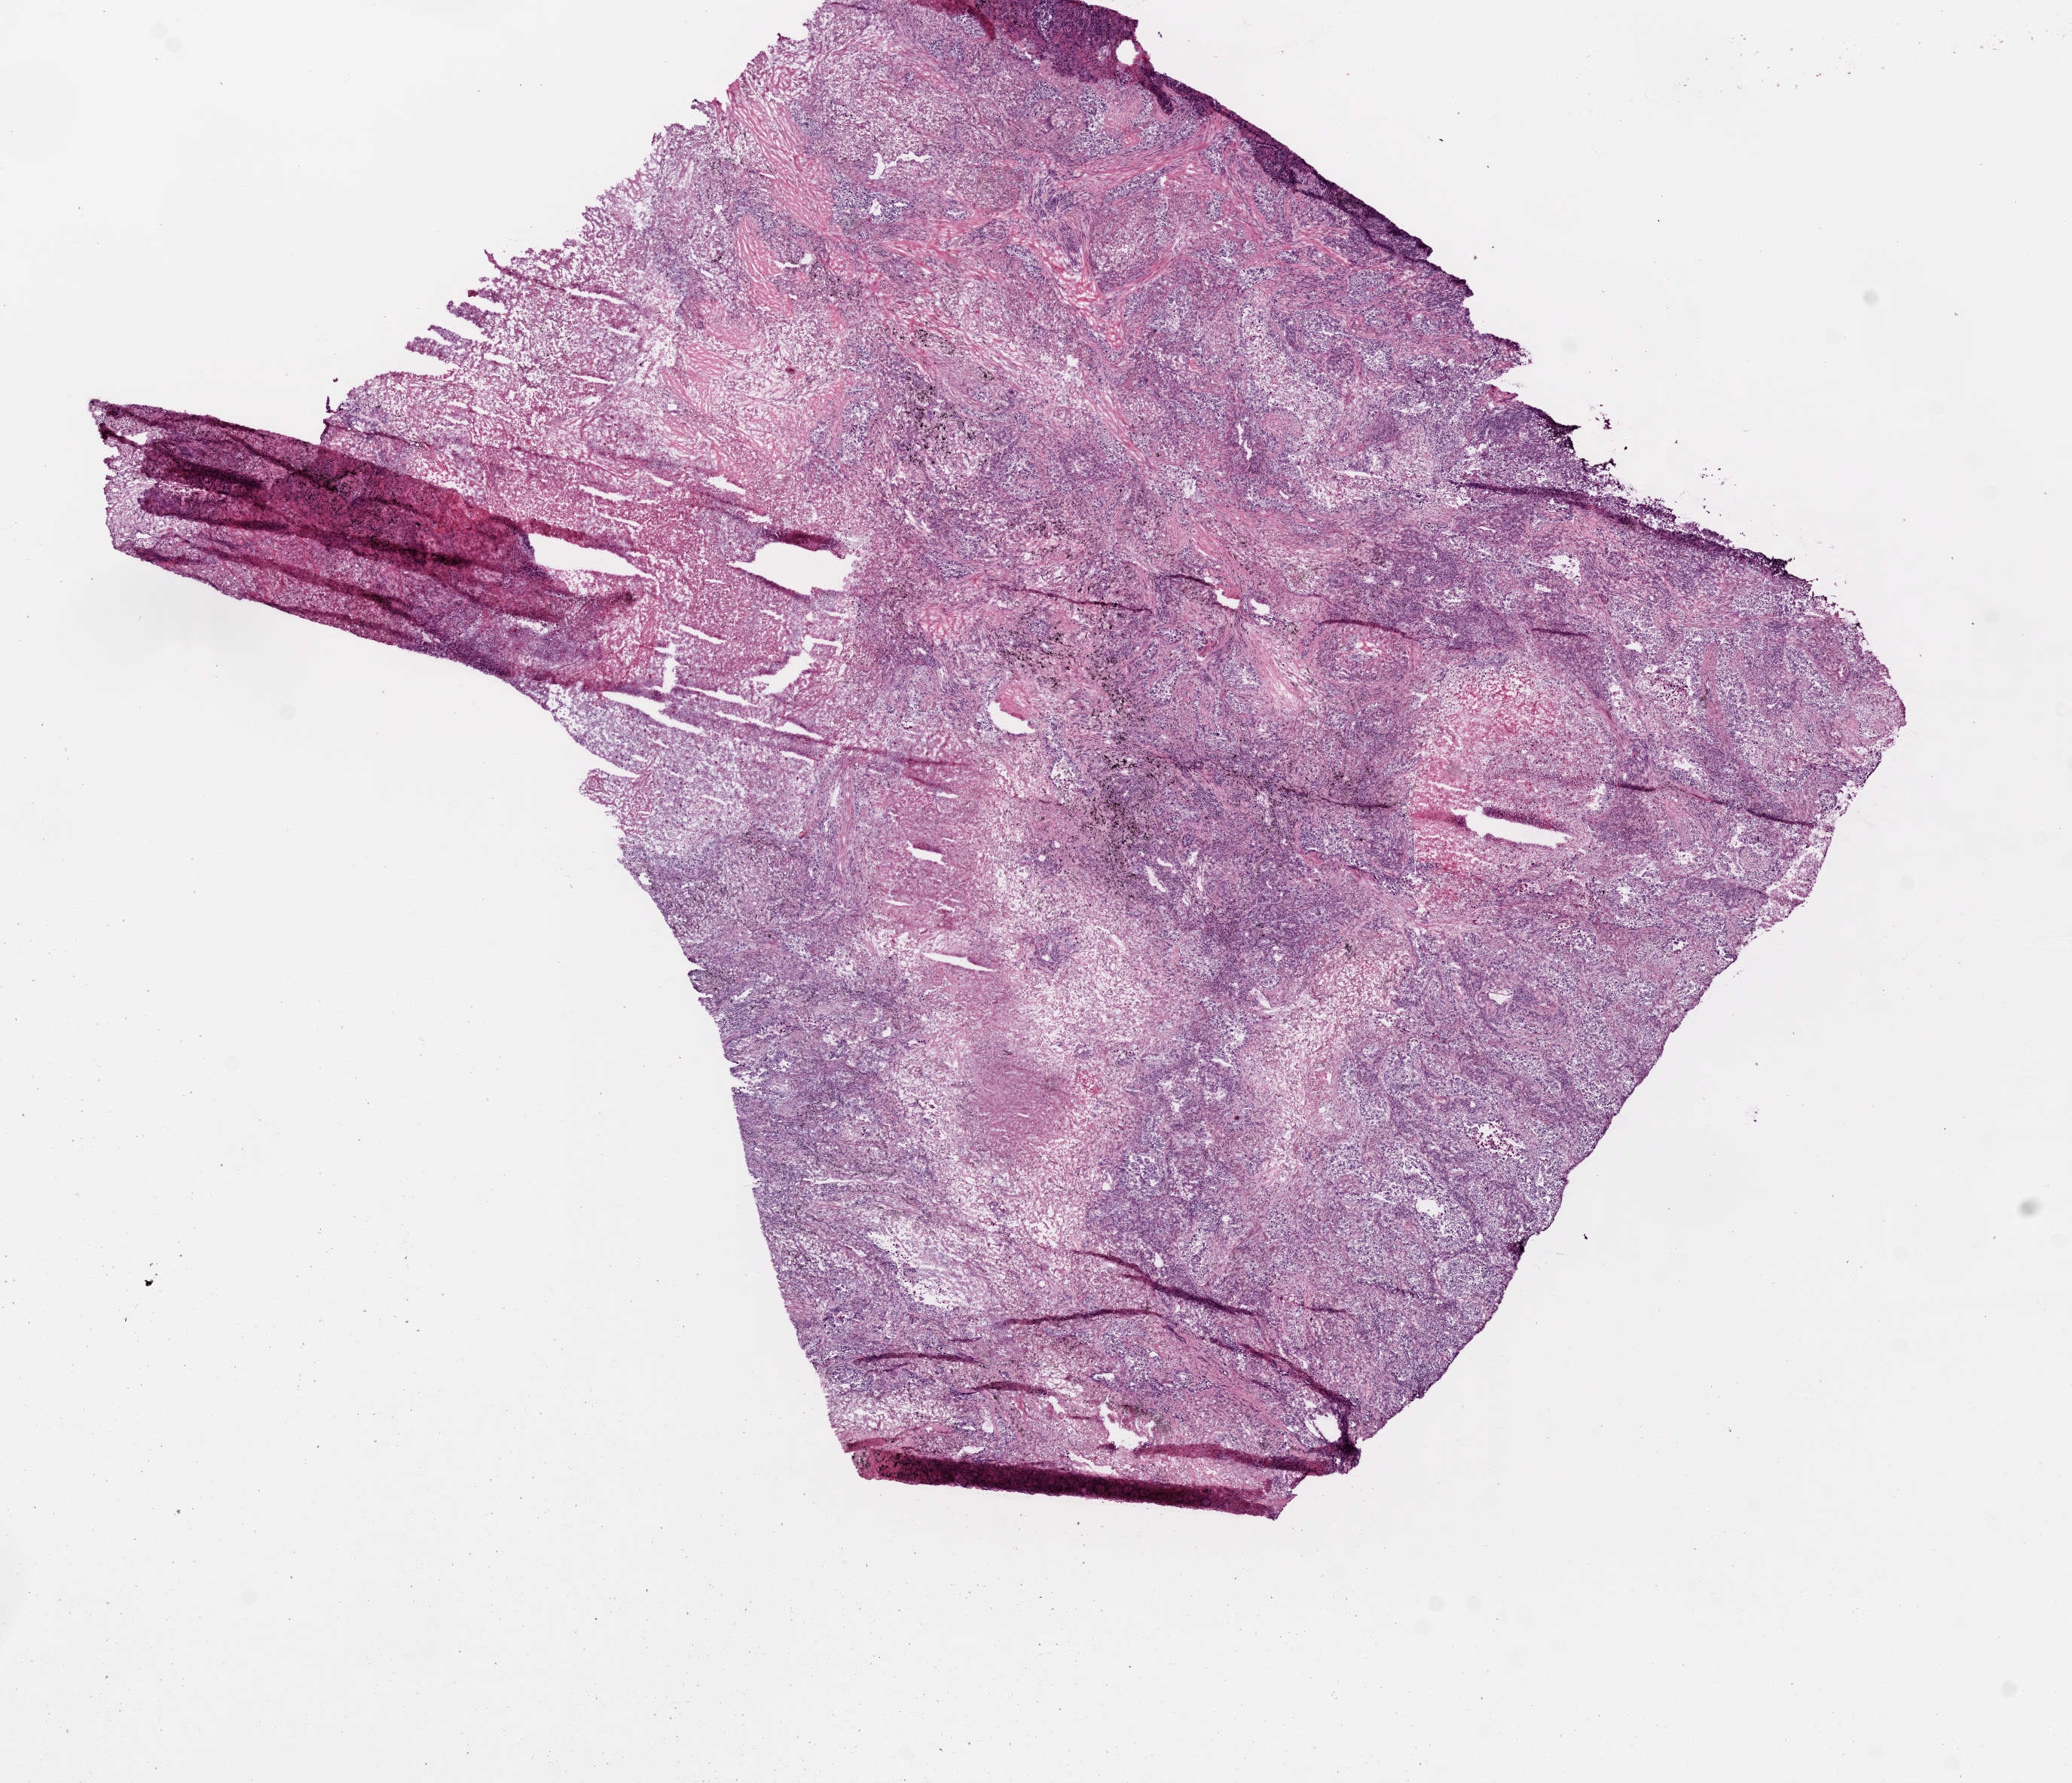
H&E-stained whole-slide image — low-resolution overview of the scanned area, about 11.0 x 9.5 mm; frozen section from the bottom of the tissue portion; lung, primary tumour sample. Male patient; age at initial diagnosis 68 years. Composition of this section per pathologist review: tumour nuclei 70%, normal cells 0%, stromal cells 10%, necrosis 20%.
- AJCC pathologic stage: IB
- pathologic diagnosis: Adenocarcinoma with mixed subtypes (upper lobe, lung)
- laterality: left